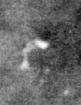
Crop from a digitized film mammogram around one marked abnormality; right breast; MLO view.
Marked abnormality: calcifications, morphology pleomorphic, distribution clustered; BI-RADS assessment category 4; subtlety rating 4 on a 1 (subtle) to 5 (obvious) scale; pathology result (as recorded, not read from the image): malignant.